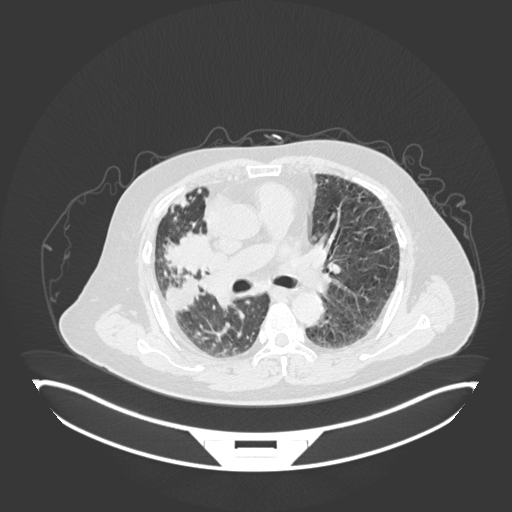
Chest CT, one axial slice. Reconstruction kernel B30f. Lung window (W 1500 / L -600 HU). 1 mm slice thickness. 512 × 512 image matrix. Male patient, age 69 years. Case-level facts recorded for this patient, not image findings: clinical TNM (as recorded): T4 N3 M1.
Annotated regions visible in this slice (bounding box drawn by a radiologist):
- lung tumour (recorded histology: adenocarcinoma): box from (x=162, y=228) to (x=220, y=286) px